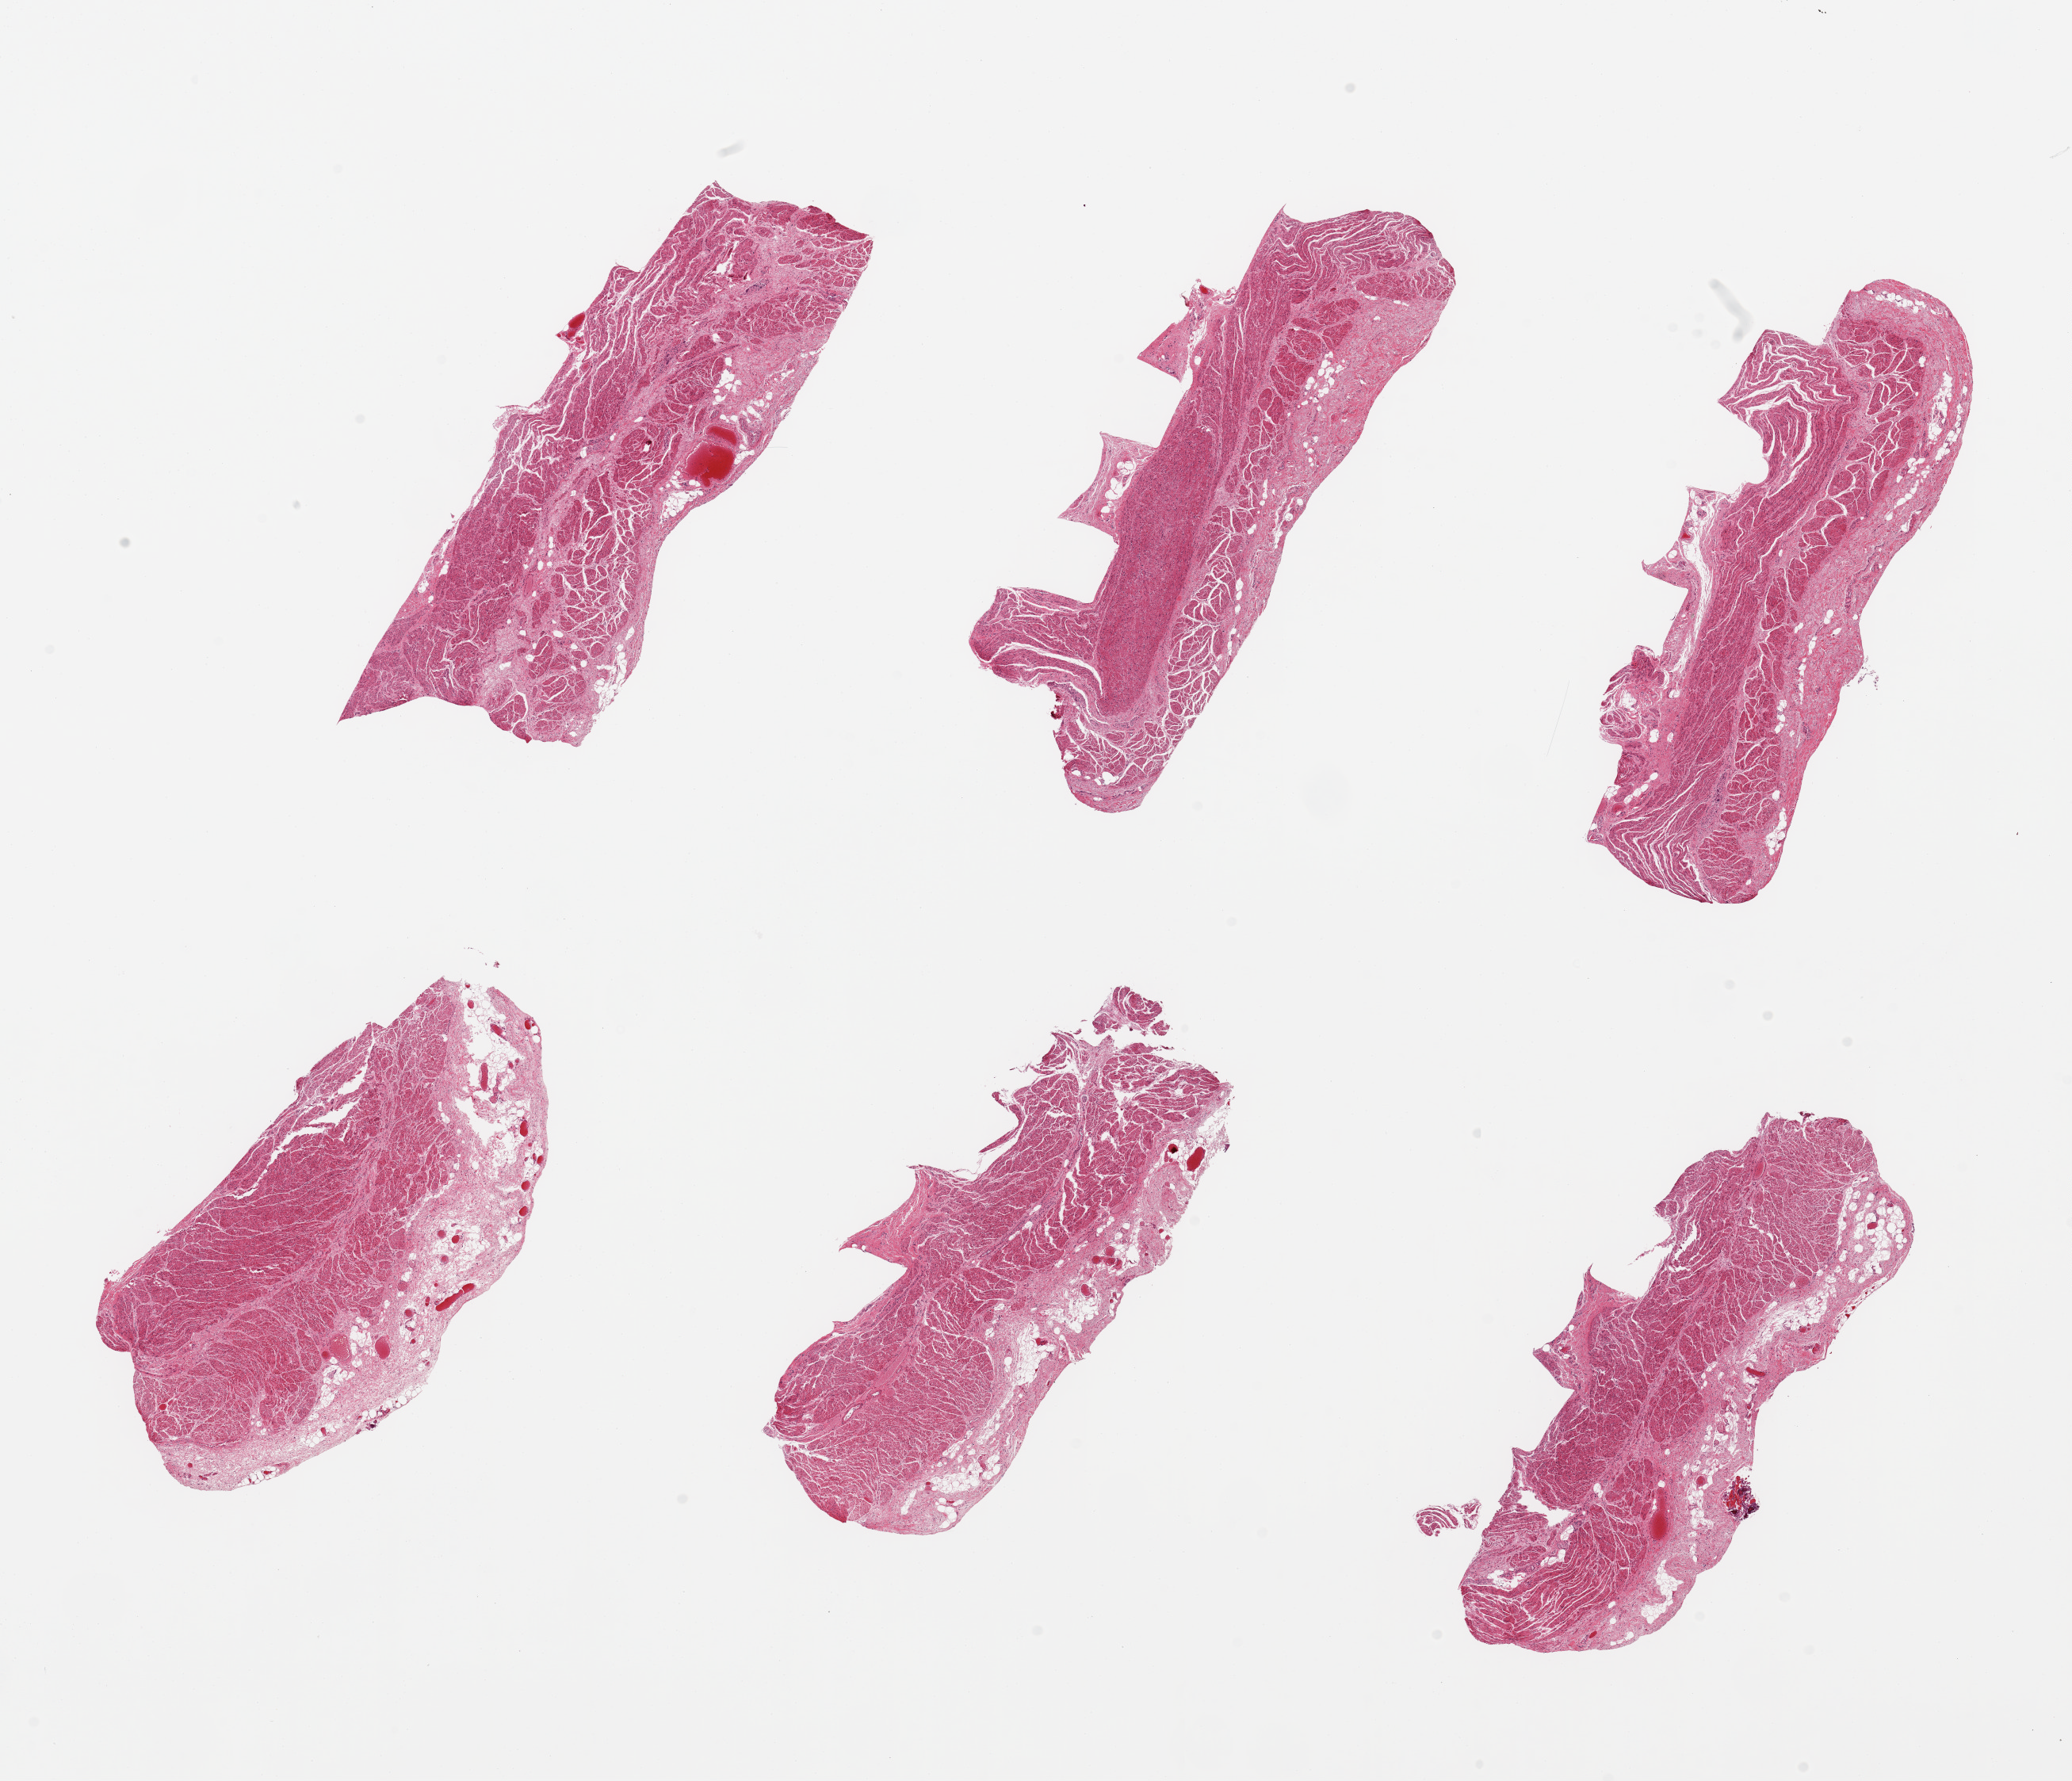
H&E whole-slide image — a low-resolution overview of the entire scanned area, about 20.7 x 17.8 mm (from a 20x scan). PAXgene-fixed paraffin-embedded (PFPE) section. Target tissue: gastroesophageal junction. Donor tissue sample. Donor: male.
- review note (as recorded): 6 pieces; target muscularis and adherent congested fibrofatty tissue up to 1 mm; fragment of skeletal muscle and calcifications